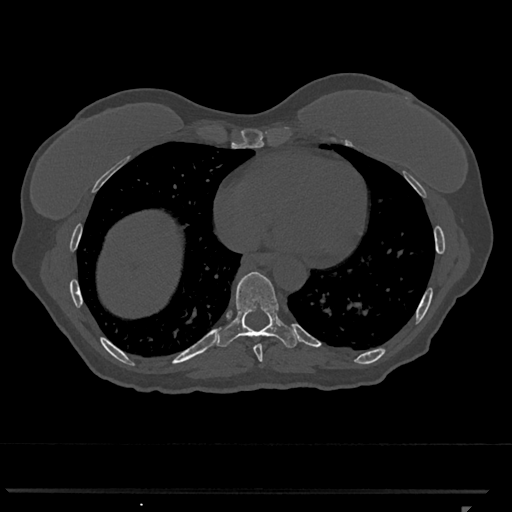
CT including the spine, one axial slice; position 628 of 793 along the scan axis; reconstruction kernel Br40s/3; 120 kVp; bone window (W 1800 / L 400 HU); 0.5 mm slice thickness; 512 × 512 image matrix, field of view 380 × 380 mm. Patient: female, 62 years. Case-level facts recorded for this patient, not image findings: primary cancer: renal.
Structures marked on this image (semi-automatic segmentation, software-assisted and operator-edited):
- T8 vertebra: box from (x=254, y=344) to (x=263, y=362) px
- T9 vertebra: (x=215, y=271)–(x=298, y=348)